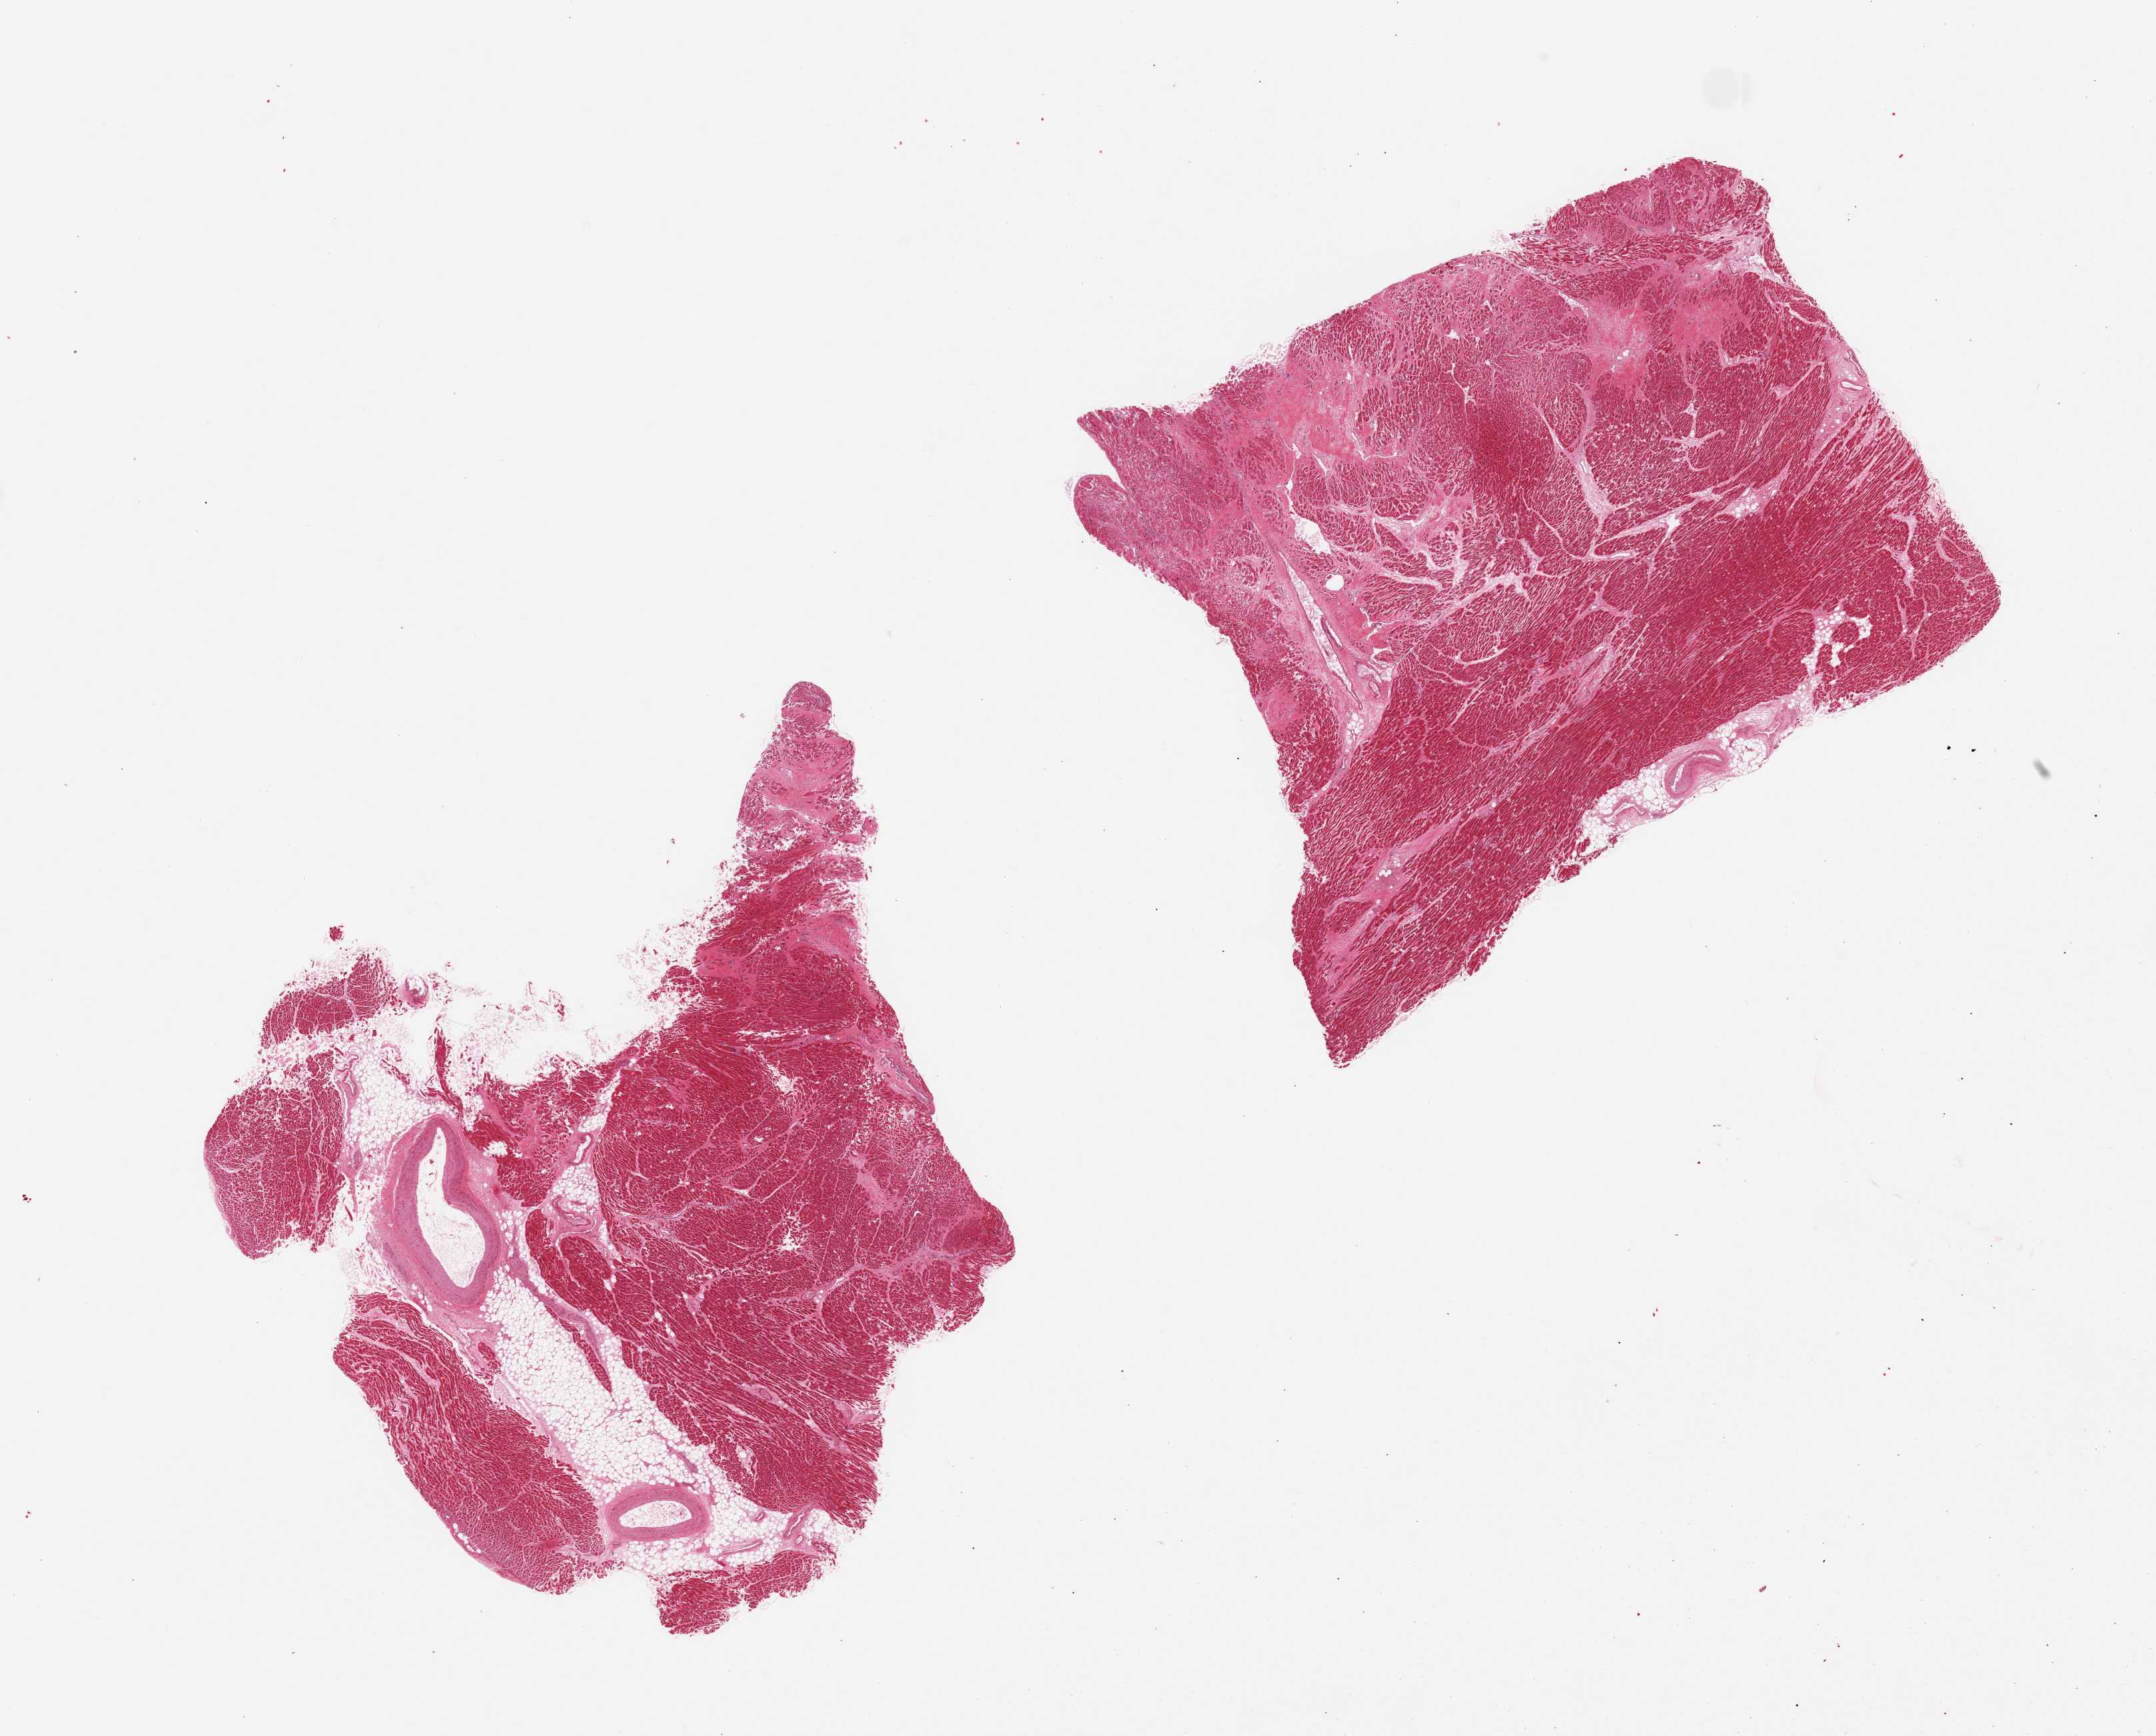
Whole-slide image, haematoxylin and eosin stain, brightfield, a low-resolution overview of the entire scanned area, about 25.6 x 20.6 mm (slide scanned at 20x). PAXgene-fixed, paraffin-embedded tissue. Target tissue: heart. Tissue donor sample. Donor: female.
Pathologist's review note for this sample: 2pieces, multifocal recent infarcts.